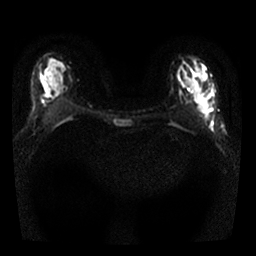
Breast MRI, one axial slice; slice 14 of 25 in the series (ordered by position); diffusion-weighted series; image 2 of 4 stored at this slice position (different b-values; order by instance number); 1.5 T; 4 mm slice thickness; 256 × 256 image matrix, field of view 300 × 300 mm. Female patient.
Outlined on this slice (outlined manually by an expert reader):
- tumour on diffusion-weighted imaging: bounding box <201,80,216,133> (left, top, right, bottom; pixels)